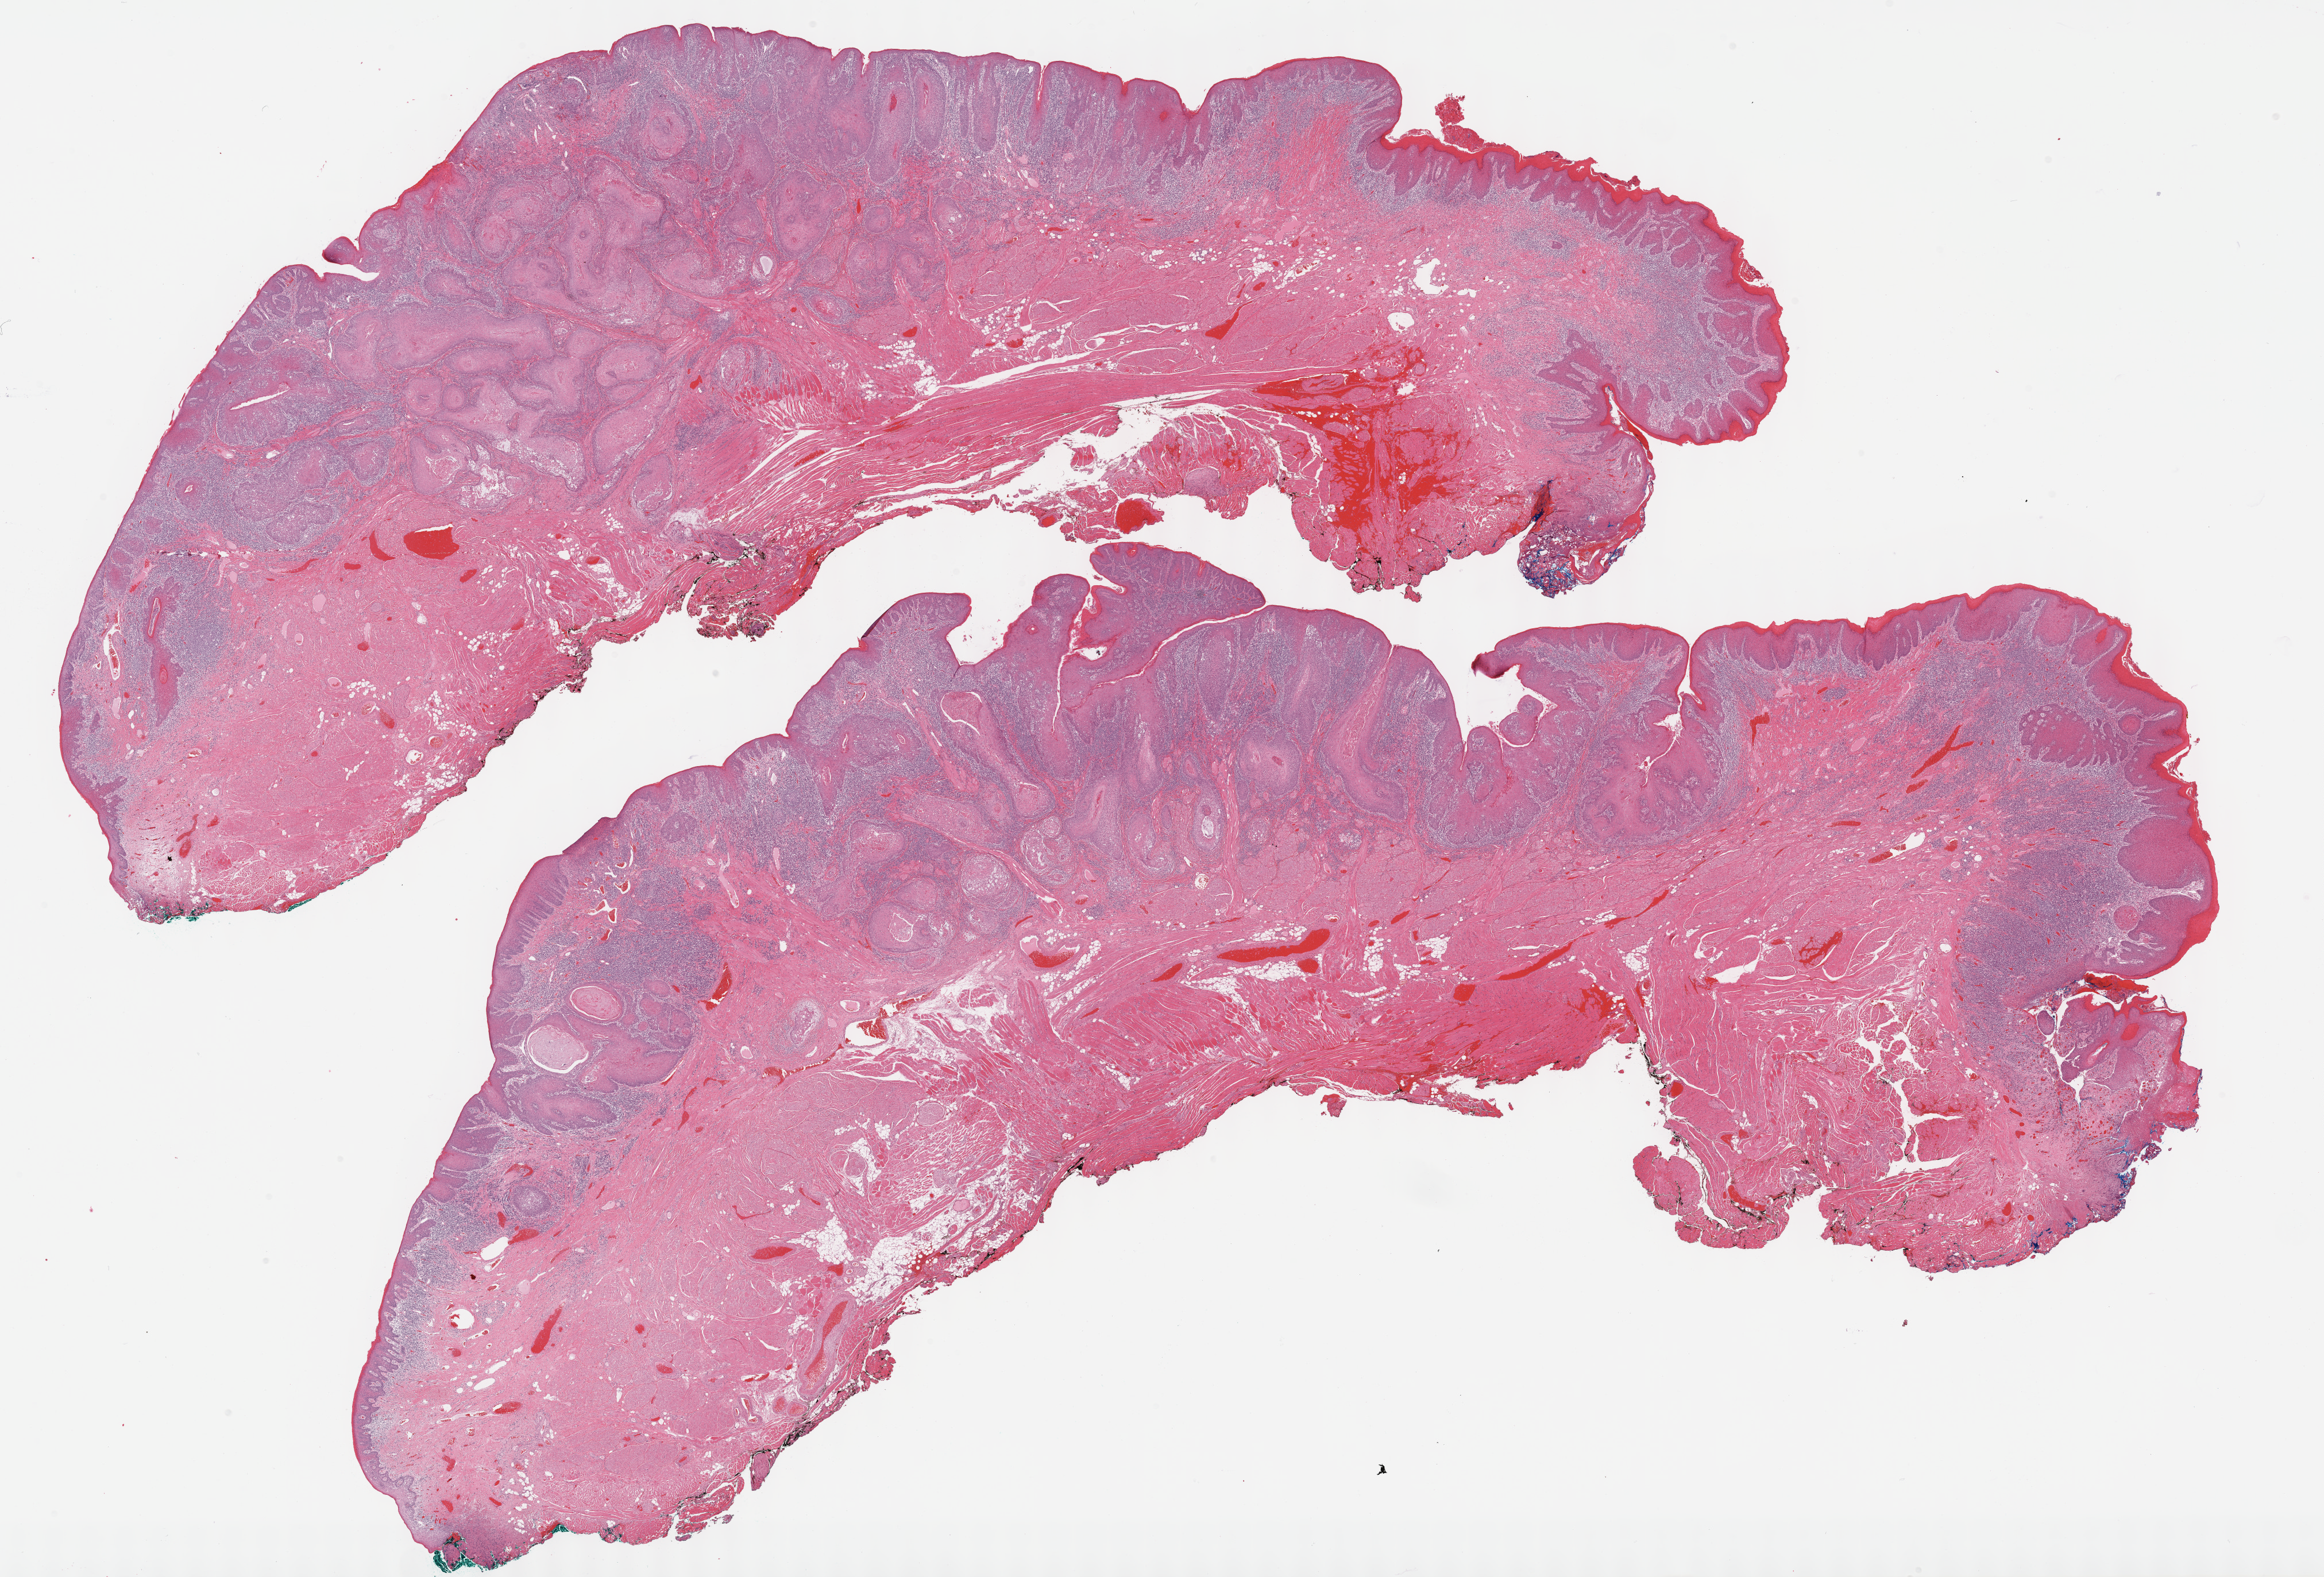
Hematoxylin and eosin (H&E) stained whole-slide image — low-resolution overview of the scanned area, about 32.7 x 22.2 mm (from a 40x scan), formalin-fixed paraffin-embedded (FFPE) diagnostic section, primary tumour sample from the head and neck. Patient: female, age at initial diagnosis 73 years. Histologic grade: G1 (well differentiated).
Histologic diagnosis: Squamous cell carcinoma, keratinizing, NOS (floor of mouth, NOS). Laterality: left.